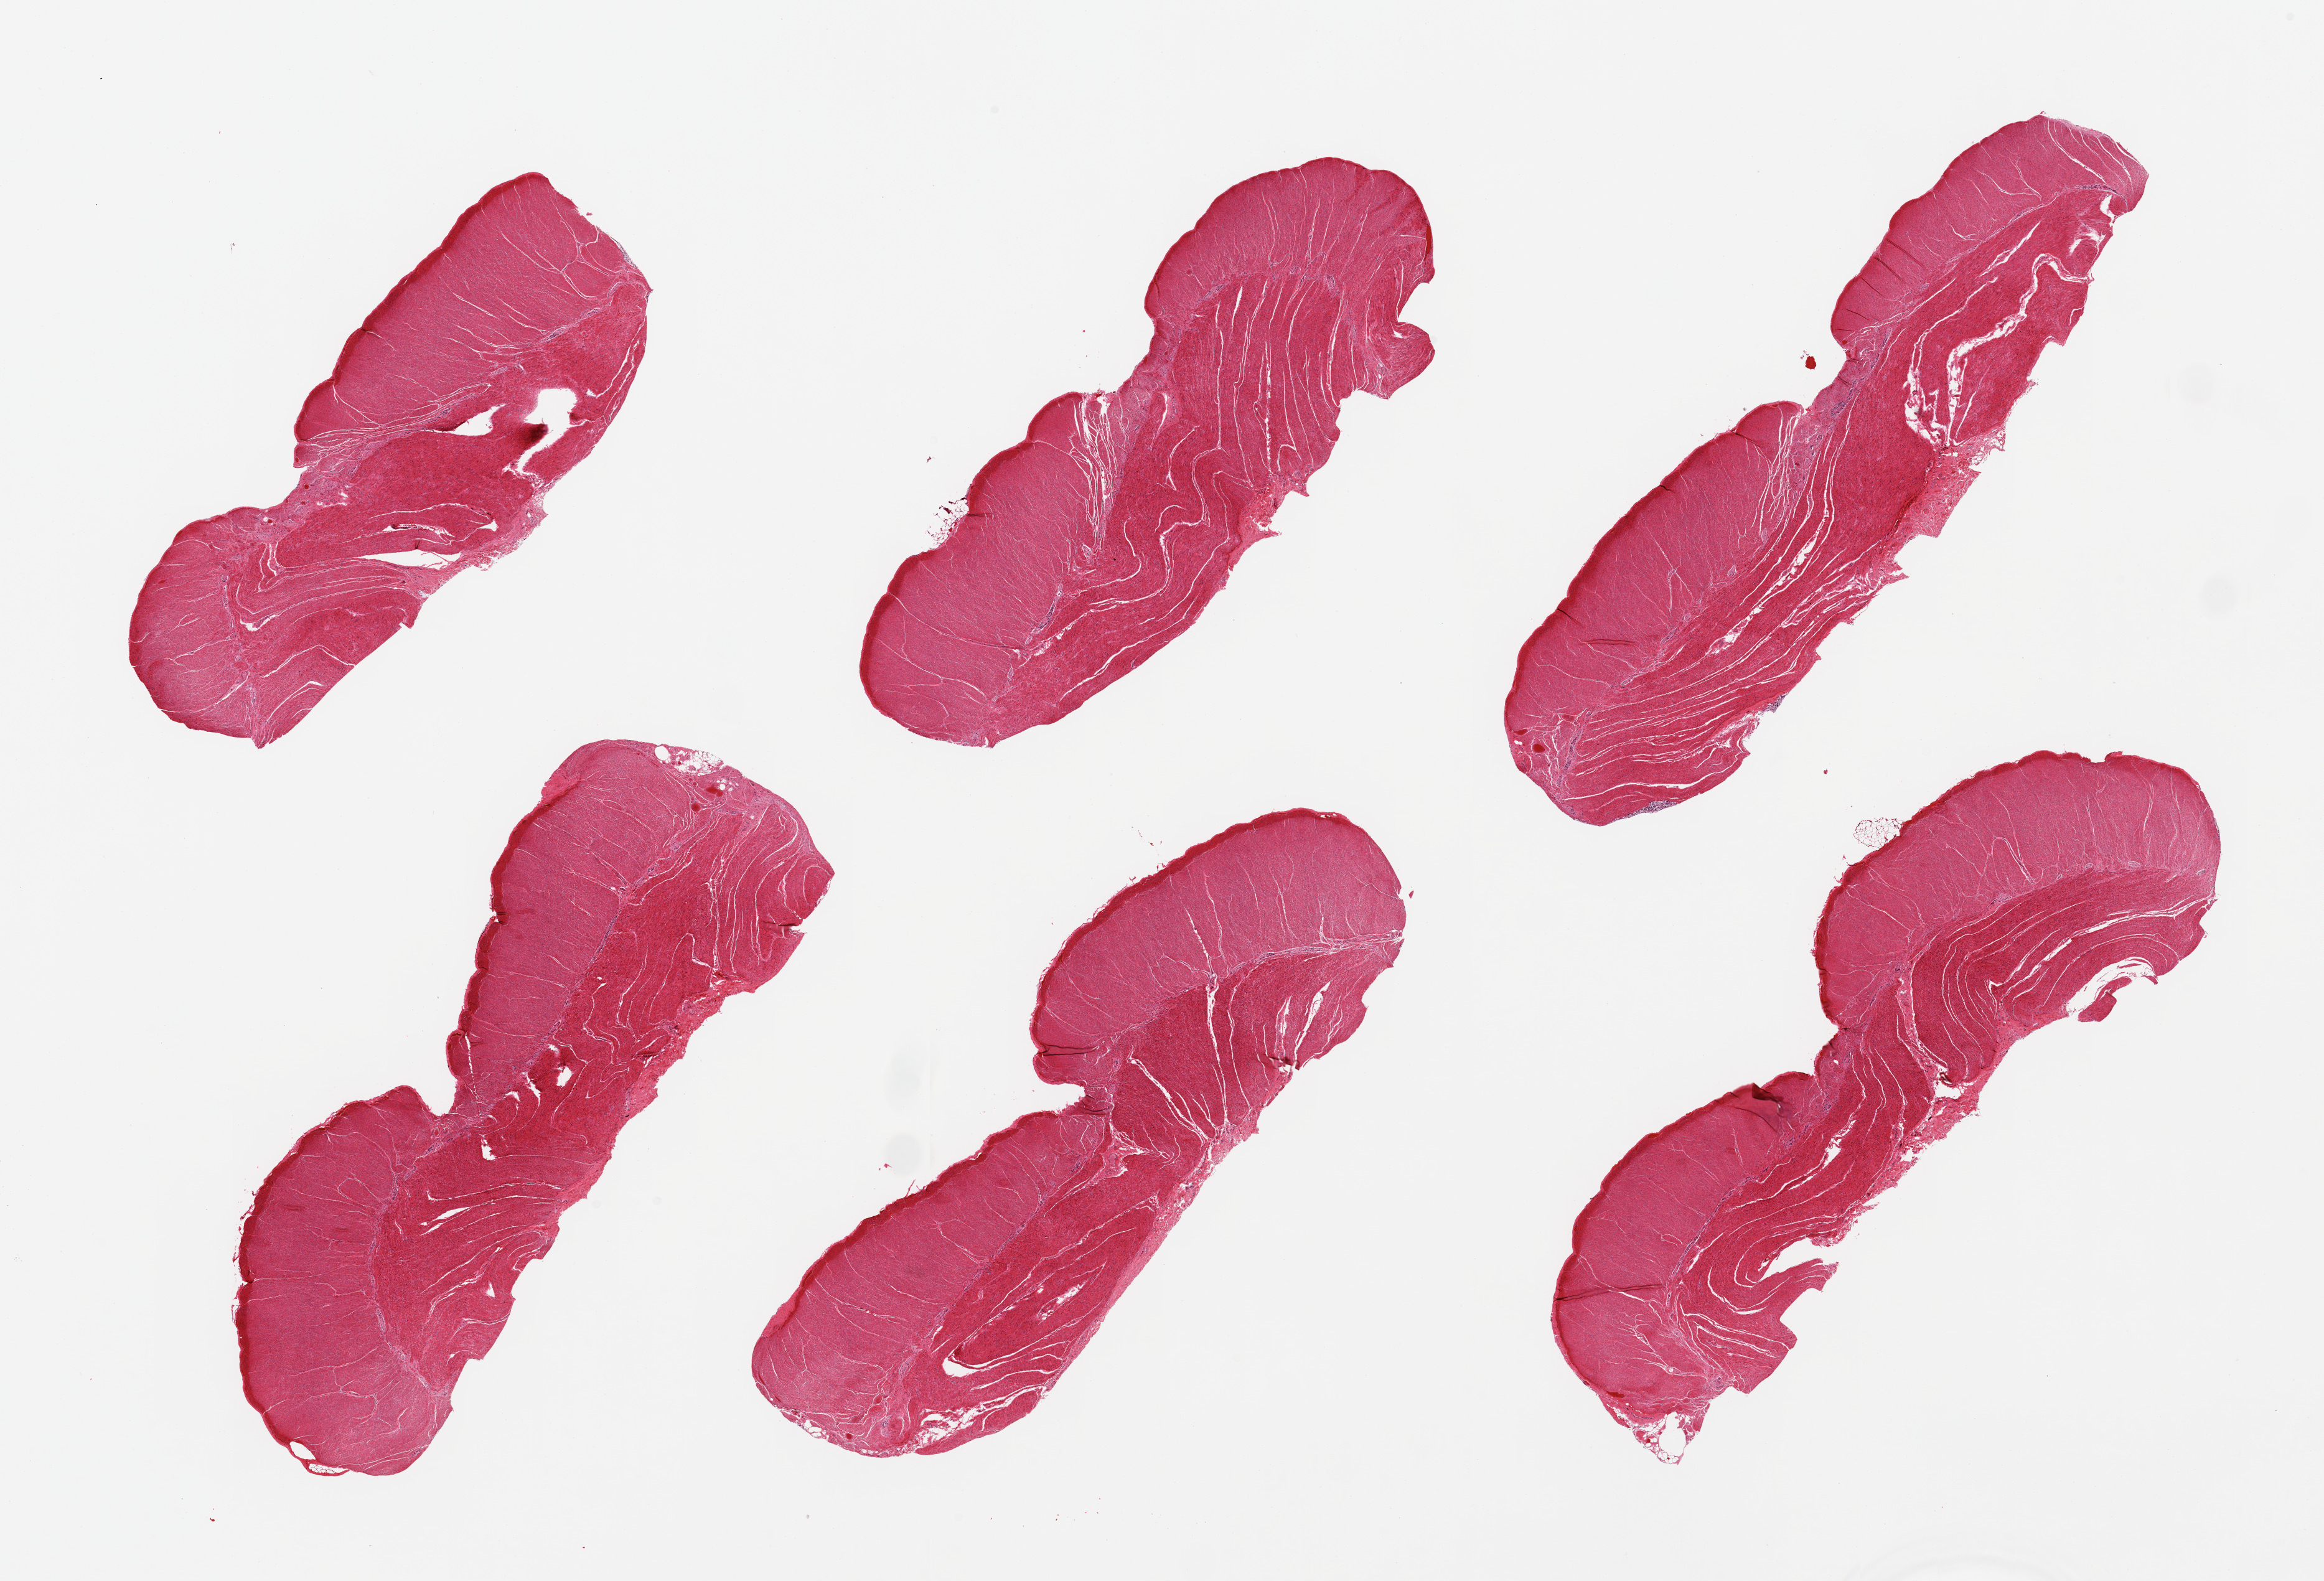
Hematoxylin and eosin (H&E) whole-slide image, brightfield — shown as a low-resolution overview of the whole scanned area (about 29.5 x 20.1 mm), PAXgene-fixed, paraffin-embedded tissue, section of sigmoid colon (target tissue), donor tissue sample. Donor sex: male.
- review note (as recorded): 6 pieces; well trimmed